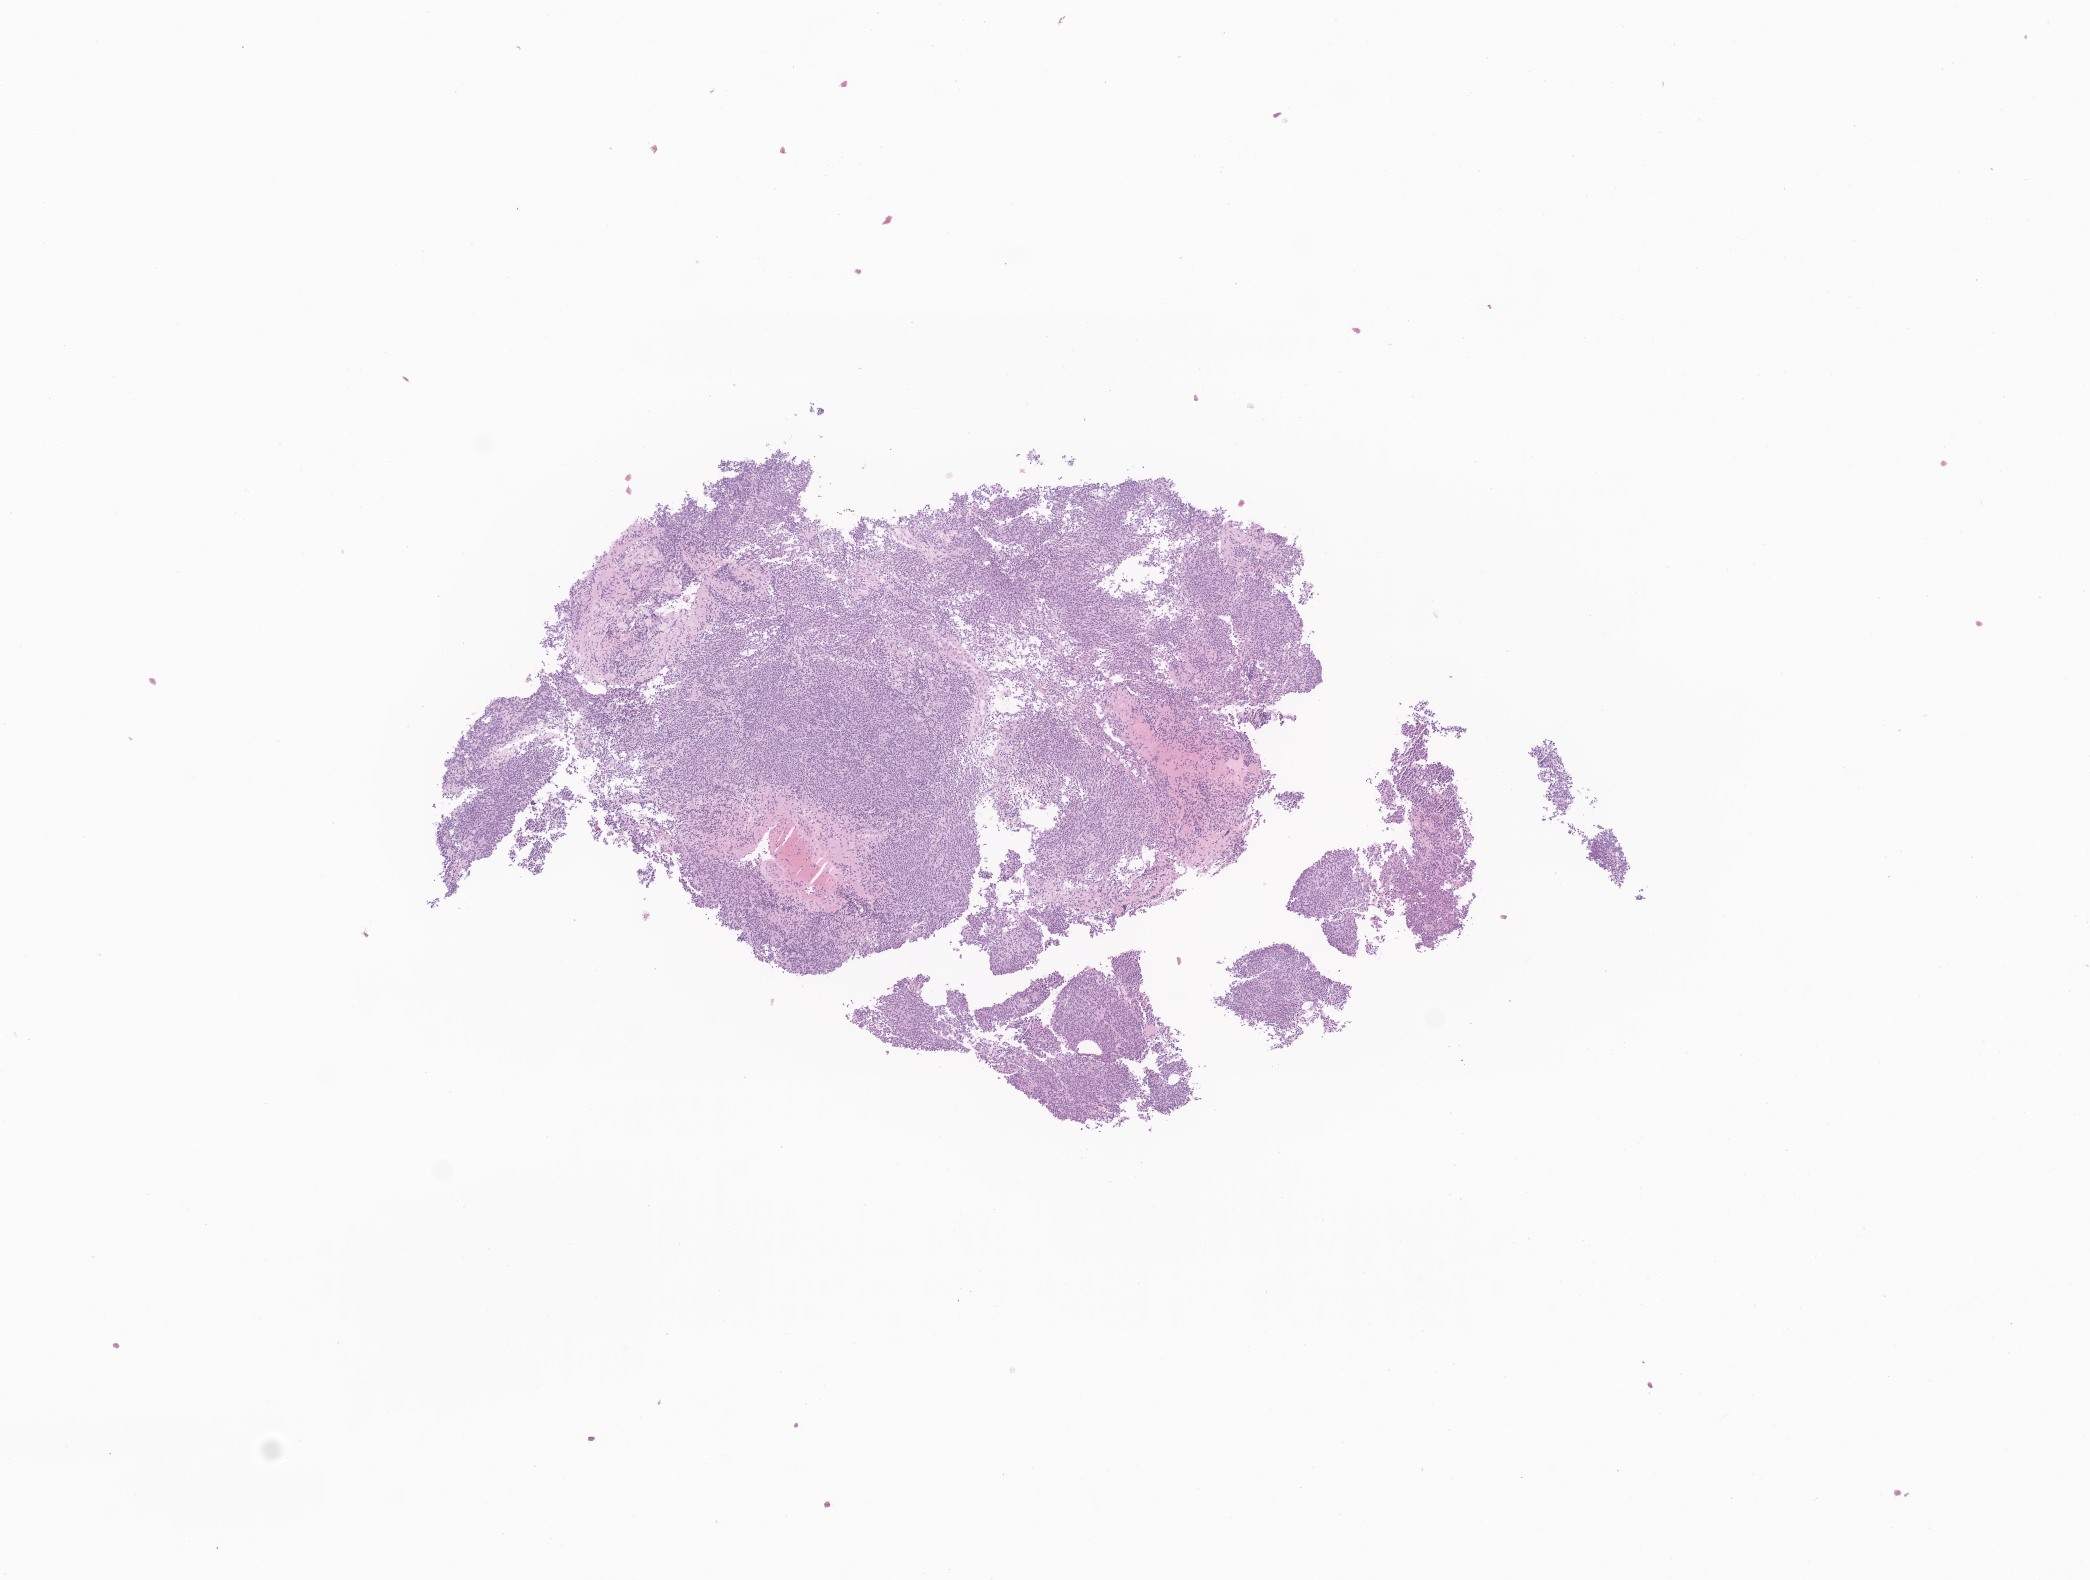
Digitized haematoxylin and eosin-stained section of tumor tissue from the brain, whole scanned area (about 8.8 x 6.7 mm) shown as a low-resolution overview; formalin-fixed, paraffin-embedded (FFPE) tissue. Female patient, age 90 months (7 years 6 months).
- diagnosis (ICD-O-3 morphology term): Medulloblastoma, NOS